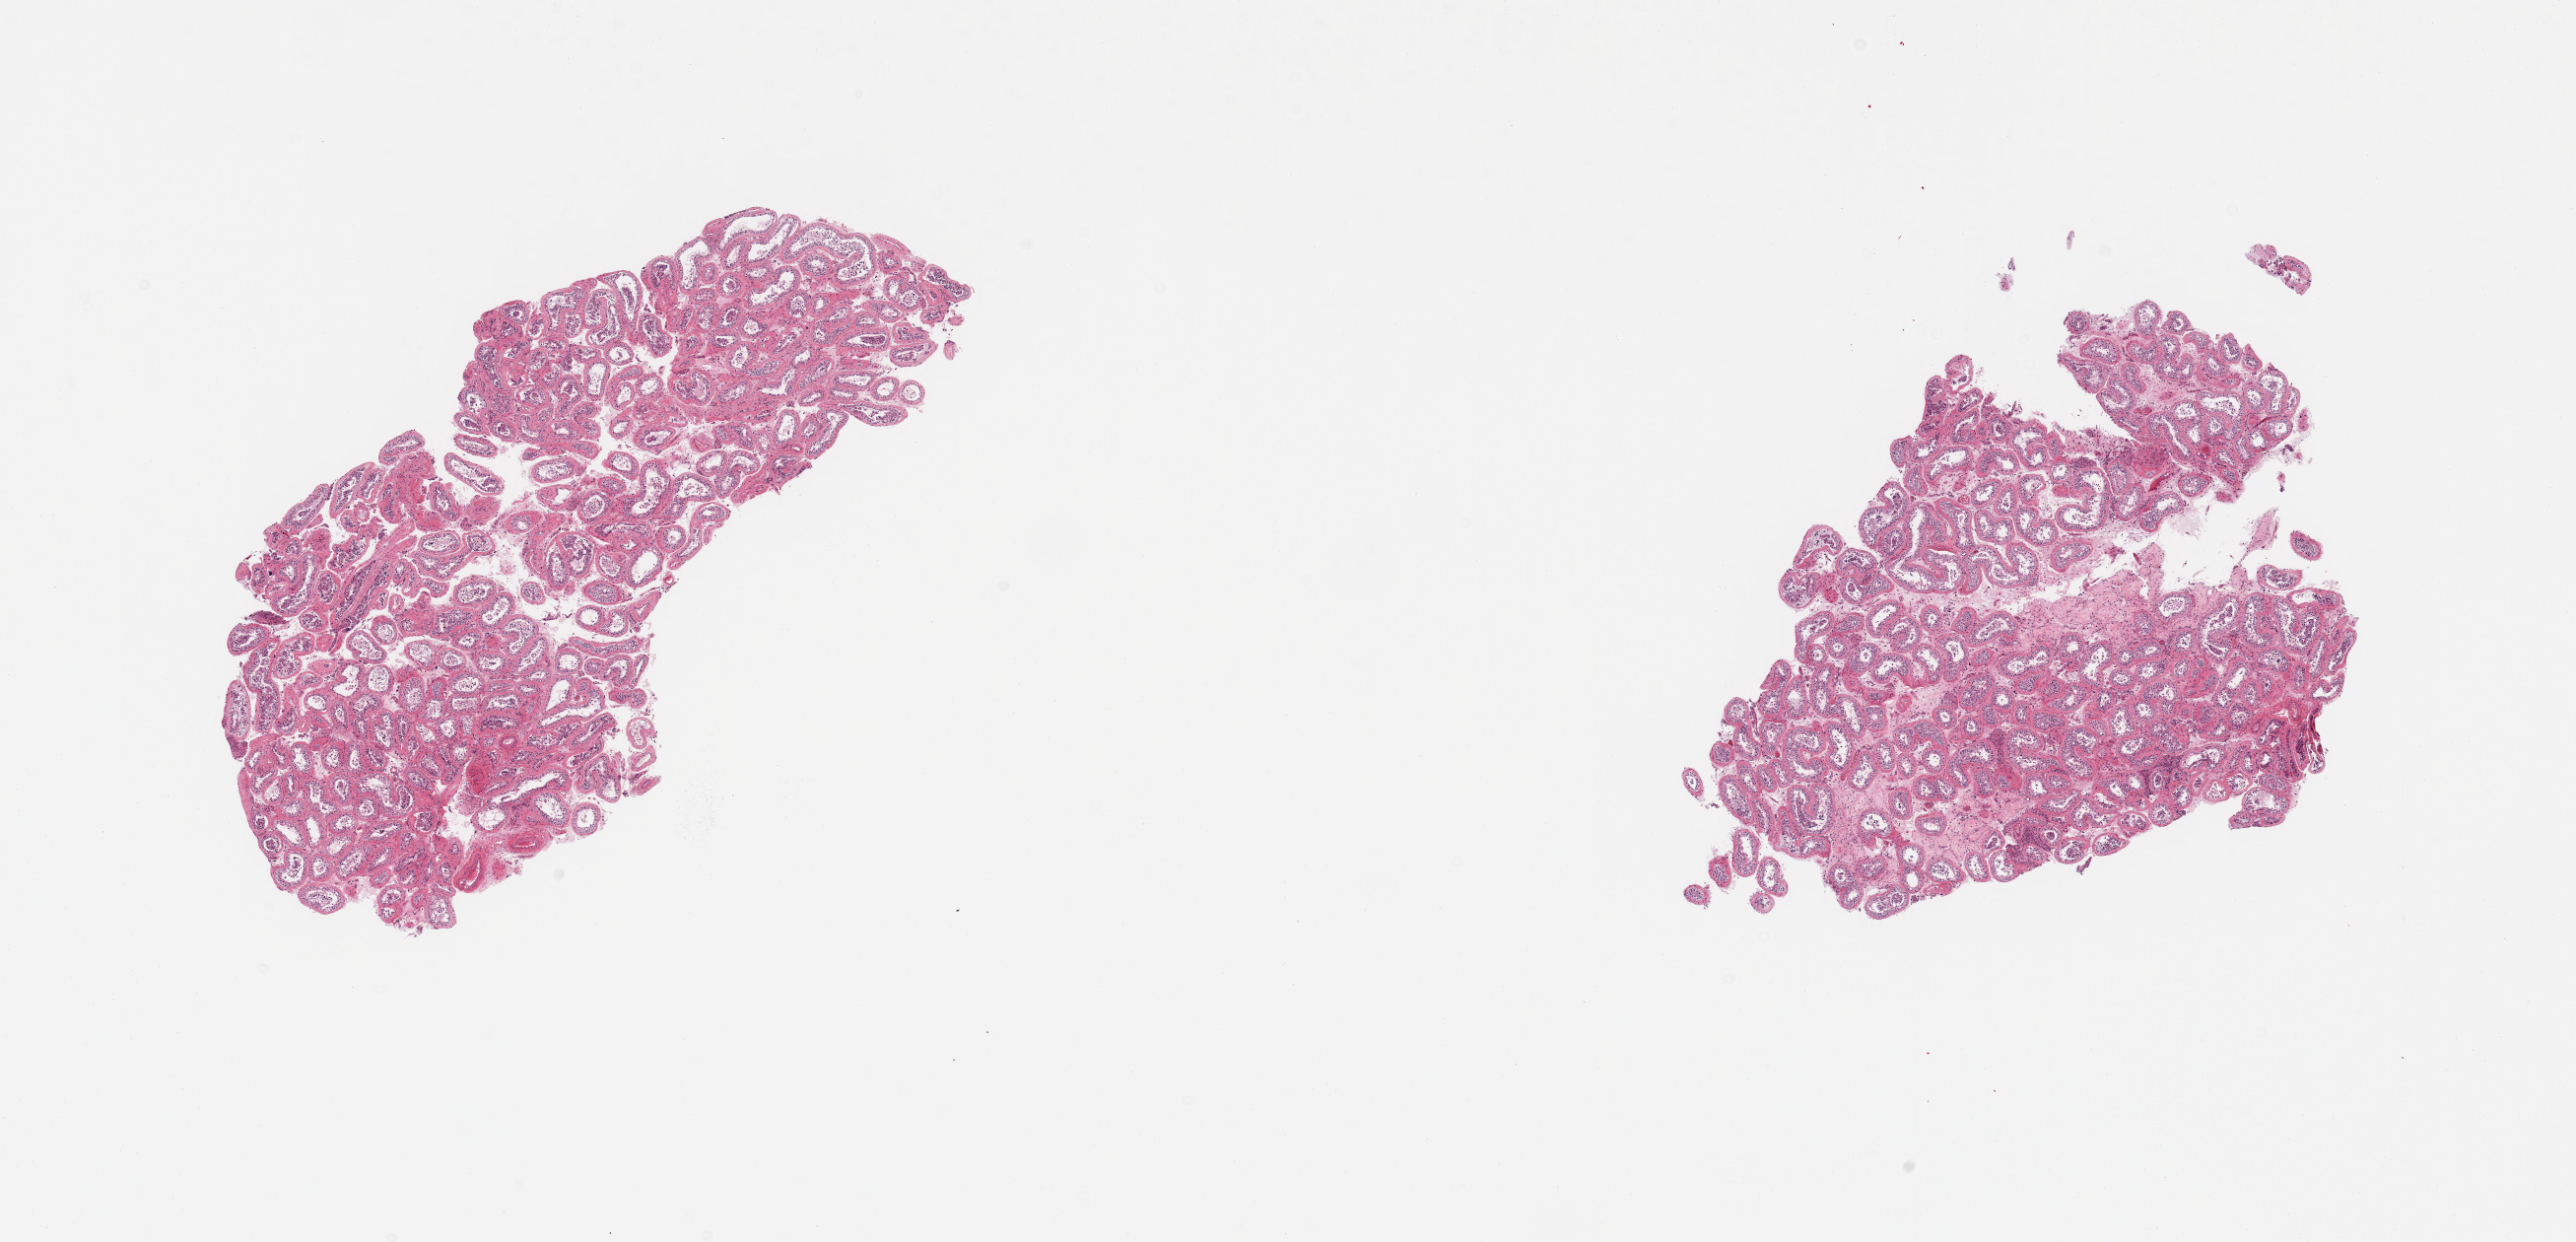
Whole-slide image, H&E stain, brightfield — shown as a low-resolution overview of the whole scanned area (about 20.7 x 10.0 mm), PAXgene-fixed, paraffin-embedded tissue, sampled site (target tissue): testis, donor tissue sample.
Review note (as recorded): 2 pieces; thickening of the basement membrane and focal hyalinization of tubules, reduced spermatogenesis.